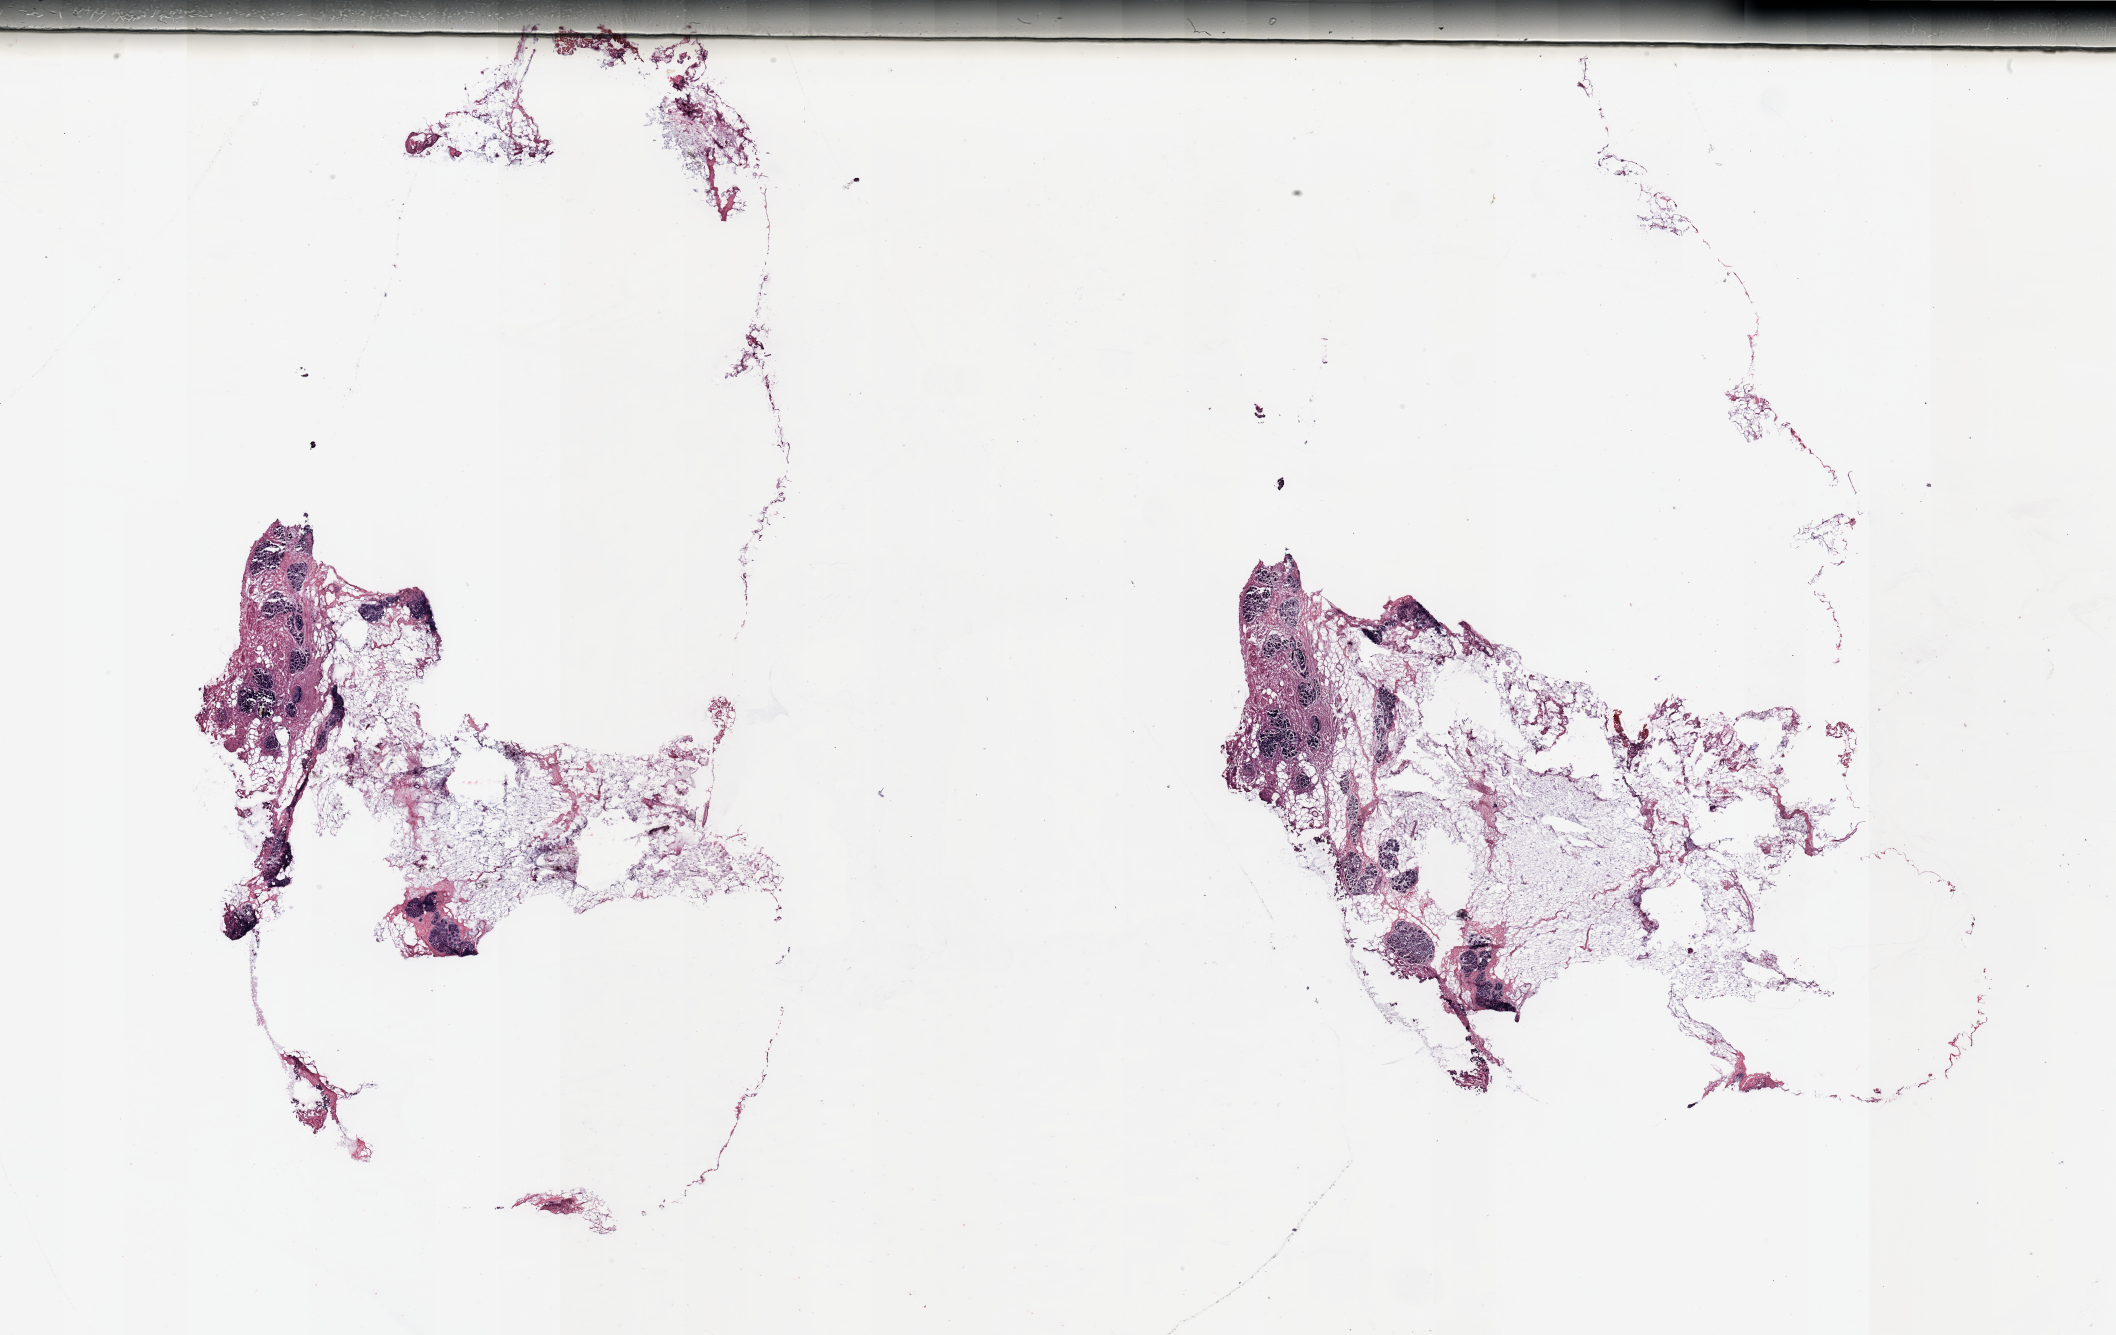
Whole-slide histology image, H&E-stained — shown as a low-resolution overview of the whole scanned area (about 33.5 x 21.1 mm, slide scanned at 20x); tumour tissue sample, breast. Patient: female, age 37 years.
Diagnosis: Infiltrating duct carcinoma, NOS. AJCC pathologic stage: IIA.